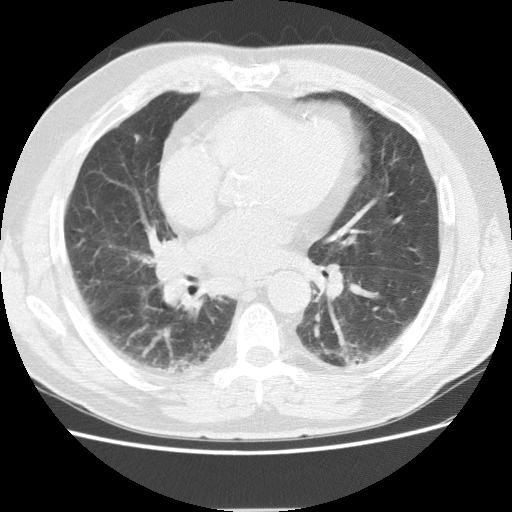
Chest CT (low-dose screening protocol), one axial image, baseline screening round, lung window (W 1500 / L -600 HU), 2.5 mm slice thickness, standard (soft-tissue) reconstruction kernel (STANDARD), 120 kVp, slice 72 of 155 in the series. Male, age 72 years at enrolment. Former smoker at enrolment.
Expert reader's lesion annotation, bounding box (x1, y1, x2, y2) in pixels: (145, 232, 195, 270). Screening reader's record for this exam: no non-calcified nodule ≥4 mm recorded. Official screen result: negative screen, minor abnormalities not suspicious for lung cancer. Participant outcome: lung cancer diagnosed 163 days after this screen — adenocarcinoma, NOS, right middle lobe, stage IIIB (AJCC 6th edition), 27 mm at pathology.